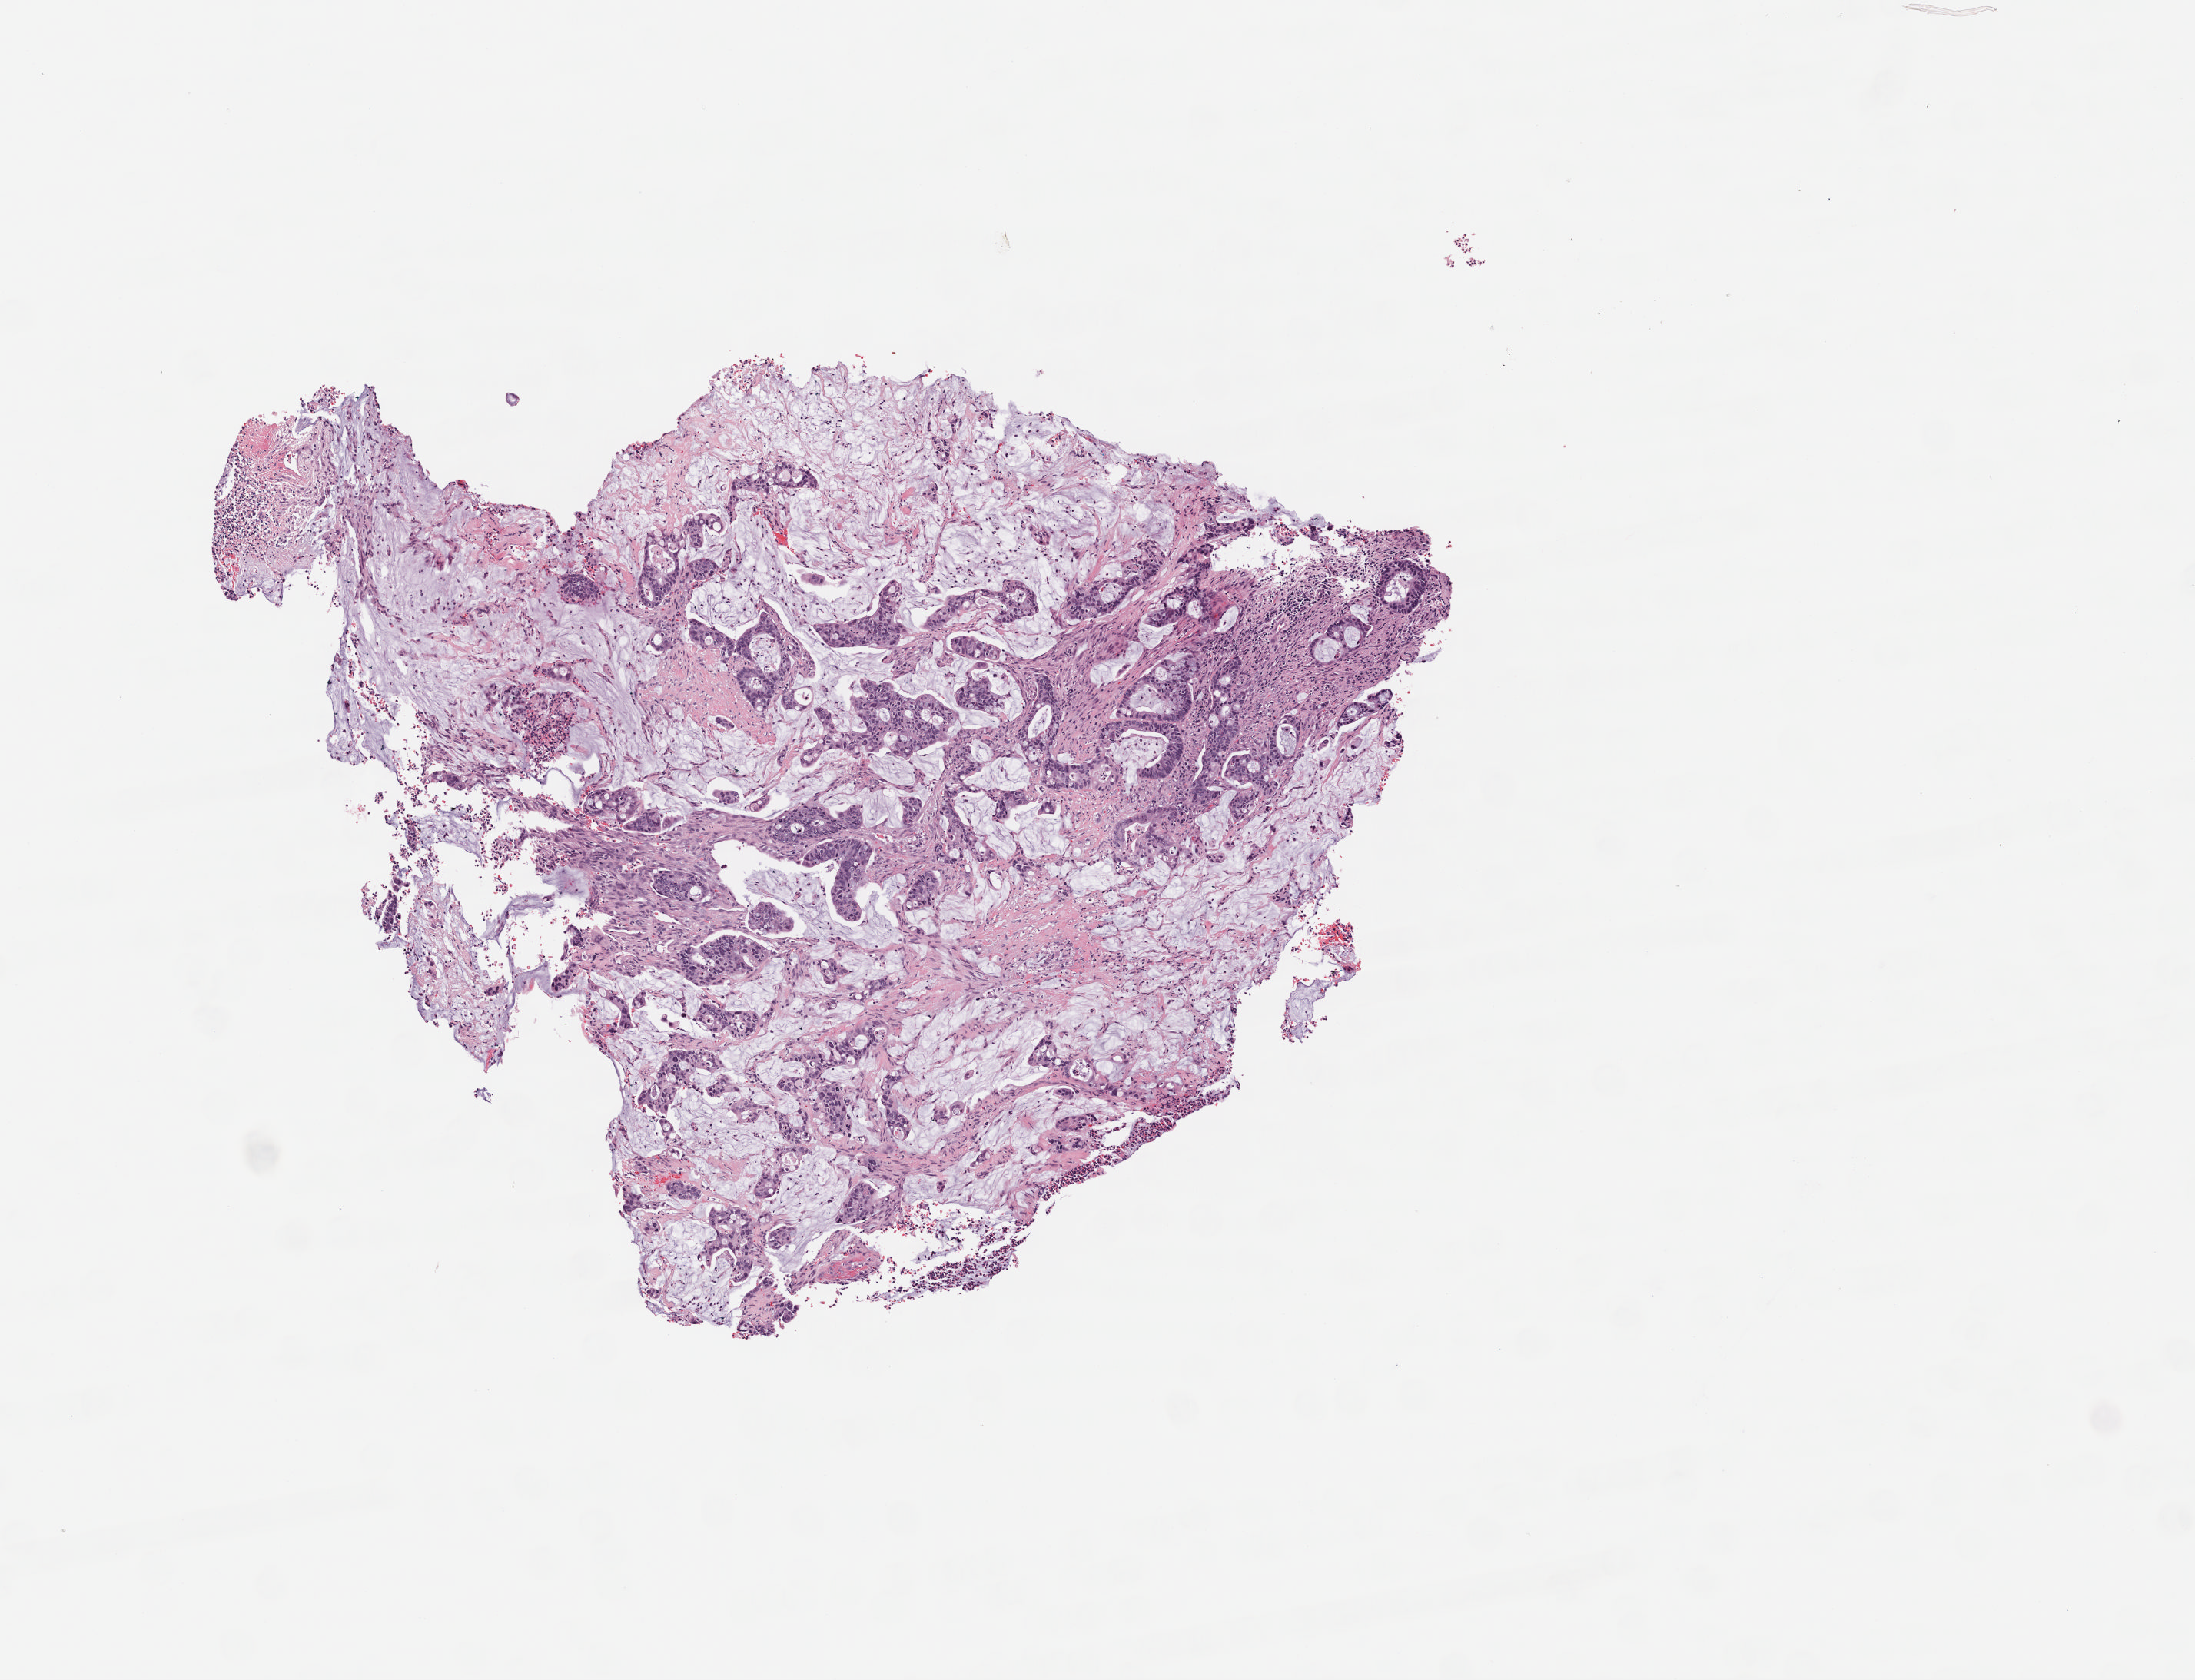
Whole-slide histology image, H&E, low-resolution overview of the scanned area, about 5.6 x 4.3 mm; frozen section from the bottom of the tissue portion; primary tumour sample from the colon. Male, age 71 years at initial diagnosis. Composition of this section per pathologist review: tumour cells 73%, tumour nuclei 68%, normal cells 0%, stromal cells 25%, necrosis 2%. Inflammatory infiltration, as recorded: lymphocyte infiltration 6%, monocyte infiltration 3%, neutrophil infiltration 15%.
- lymph nodes positive (case pathology): 7 of 20 examined
- AJCC pathologic stage: IV (6th edition)
- pathologic diagnosis: Mucinous adenocarcinoma (sigmoid colon)